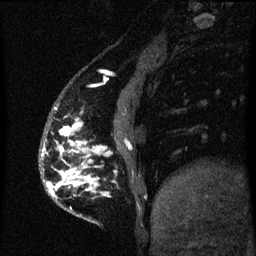
Breast MRI (dynamic contrast-enhanced), one sagittal slice; position 14 of 60 along the scan axis; dynamic contrast-enhanced series, image 2 of 3 at this slice position (ordered by acquisition); 1.5 T; TE 4.2 ms, TR 8 ms; 2 mm slice thickness; 256 × 256 image matrix. Female patient, age 50 years.
Structures marked on this image (semi-automatic segmentation, software-assisted and operator-edited):
- analysis volume of interest (the breast-tissue region the enhancement analysis was run in; not a lesion): bounding box (x1, y1, x2, y2) in pixels: (42, 122, 99, 219)
- tumour enhancement mask (voxels above the 70 % enhancement threshold inside the analysis volume of interest): (47, 123, 99, 195)